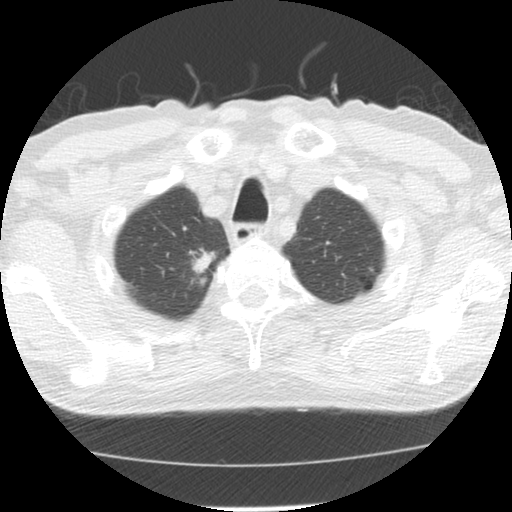
Axial slice from a low-dose chest CT screening exam. First (baseline) screen. Lung window (W 1500 / L -600 HU). 2.5 mm slice thickness. Male participant, aged 64 years at enrolment. Former smoker at enrolment.
• Lesion marked by an expert reader, bounding box <180,241,224,282> (left, top, right, bottom; pixels).
• The exam's reader record, not a measurement of the box and not confirmed to be the same lesion: non-calcified nodule or mass ≥4 mm, right upper lobe, 20 × 13 mm, spiculated (stellate) margins, soft tissue attenuation.
• Official screen result: positive, change unspecified: nodule(s) >= 4 mm or enlarging nodule(s), mass(es), or other non-specific abnormalities suspicious for lung cancer.